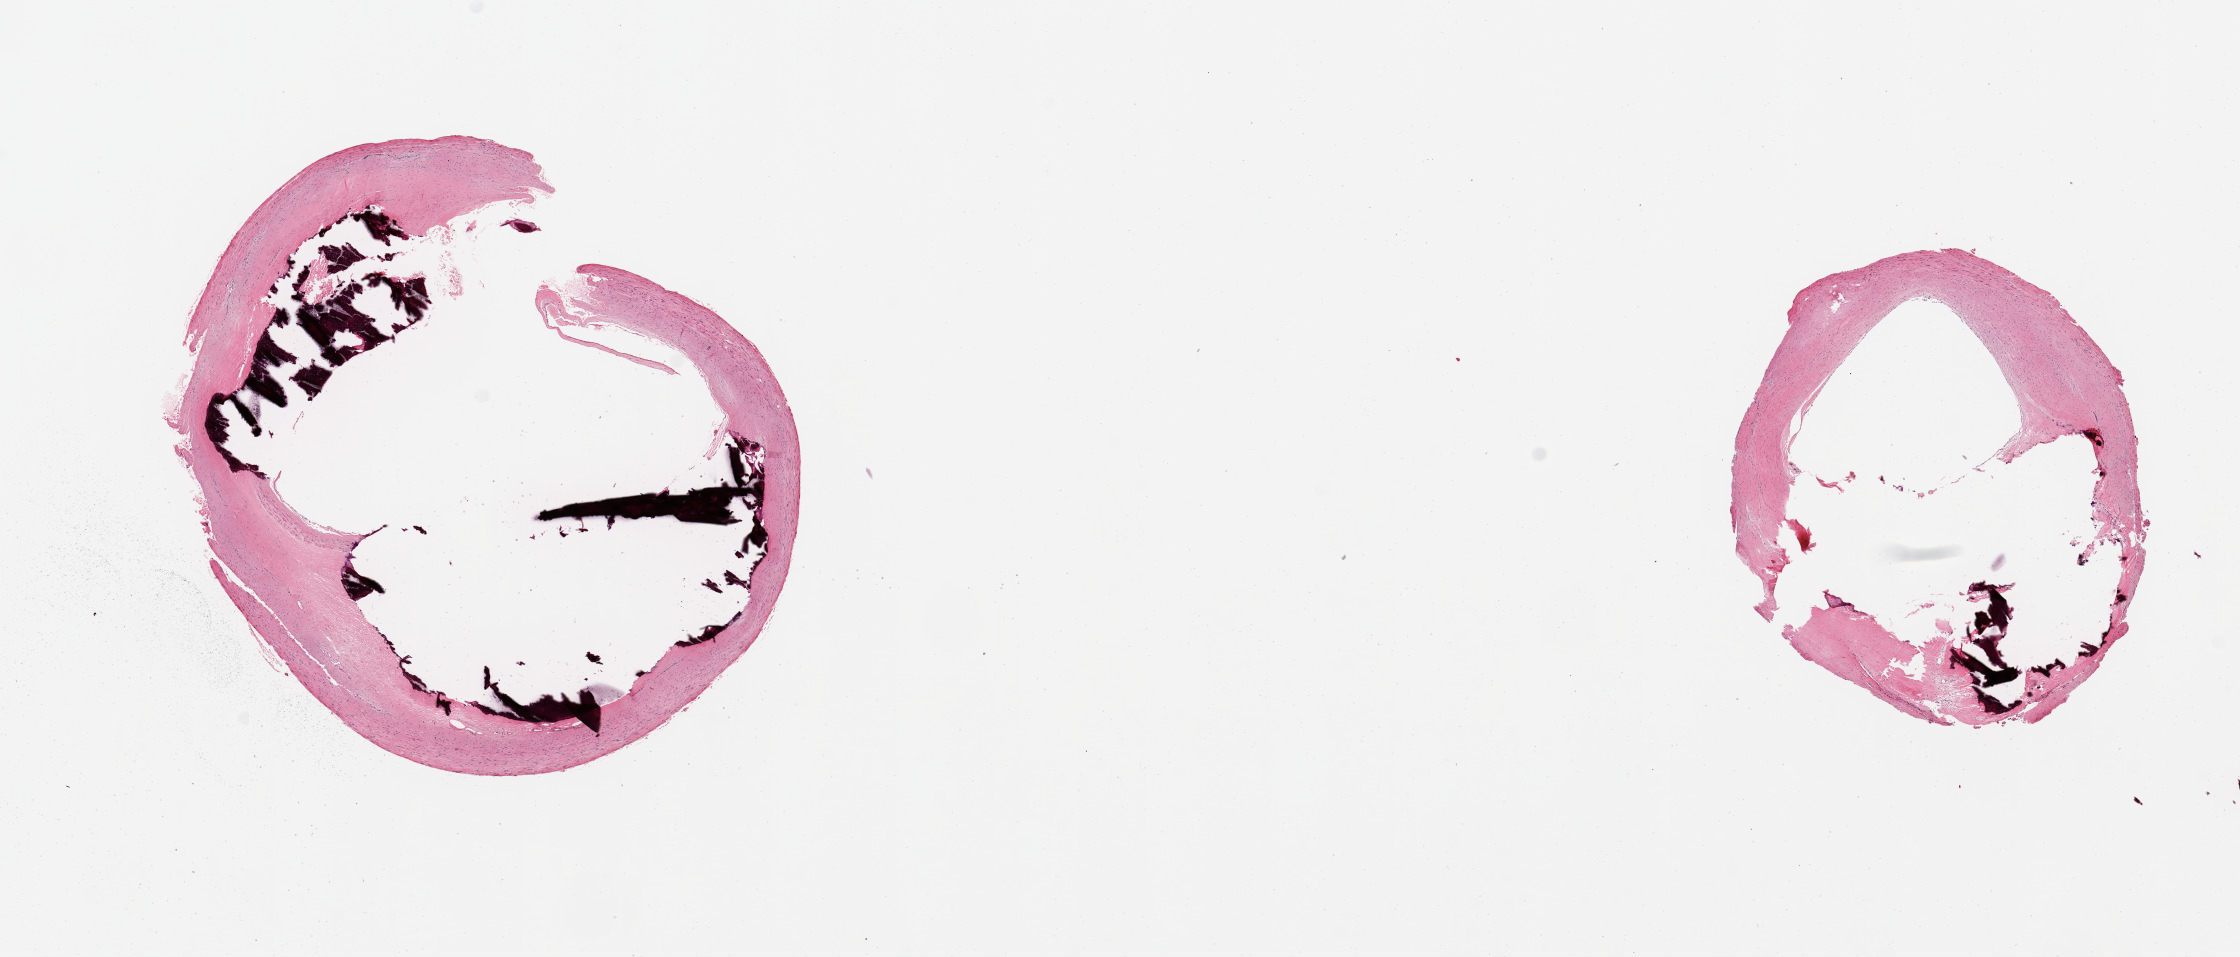
Whole-slide image, H&E stain, brightfield — low-resolution overview of the scanned area, about 17.7 x 7.6 mm (from a 20x scan), PAXgene-fixed paraffin-embedded (PFPE) section, section of coronary artery (target tissue), tissue donor sample.
Reviewer comment on this tissue sample: 2 pieces, occlusive atherosis up to ~50%, calcified.